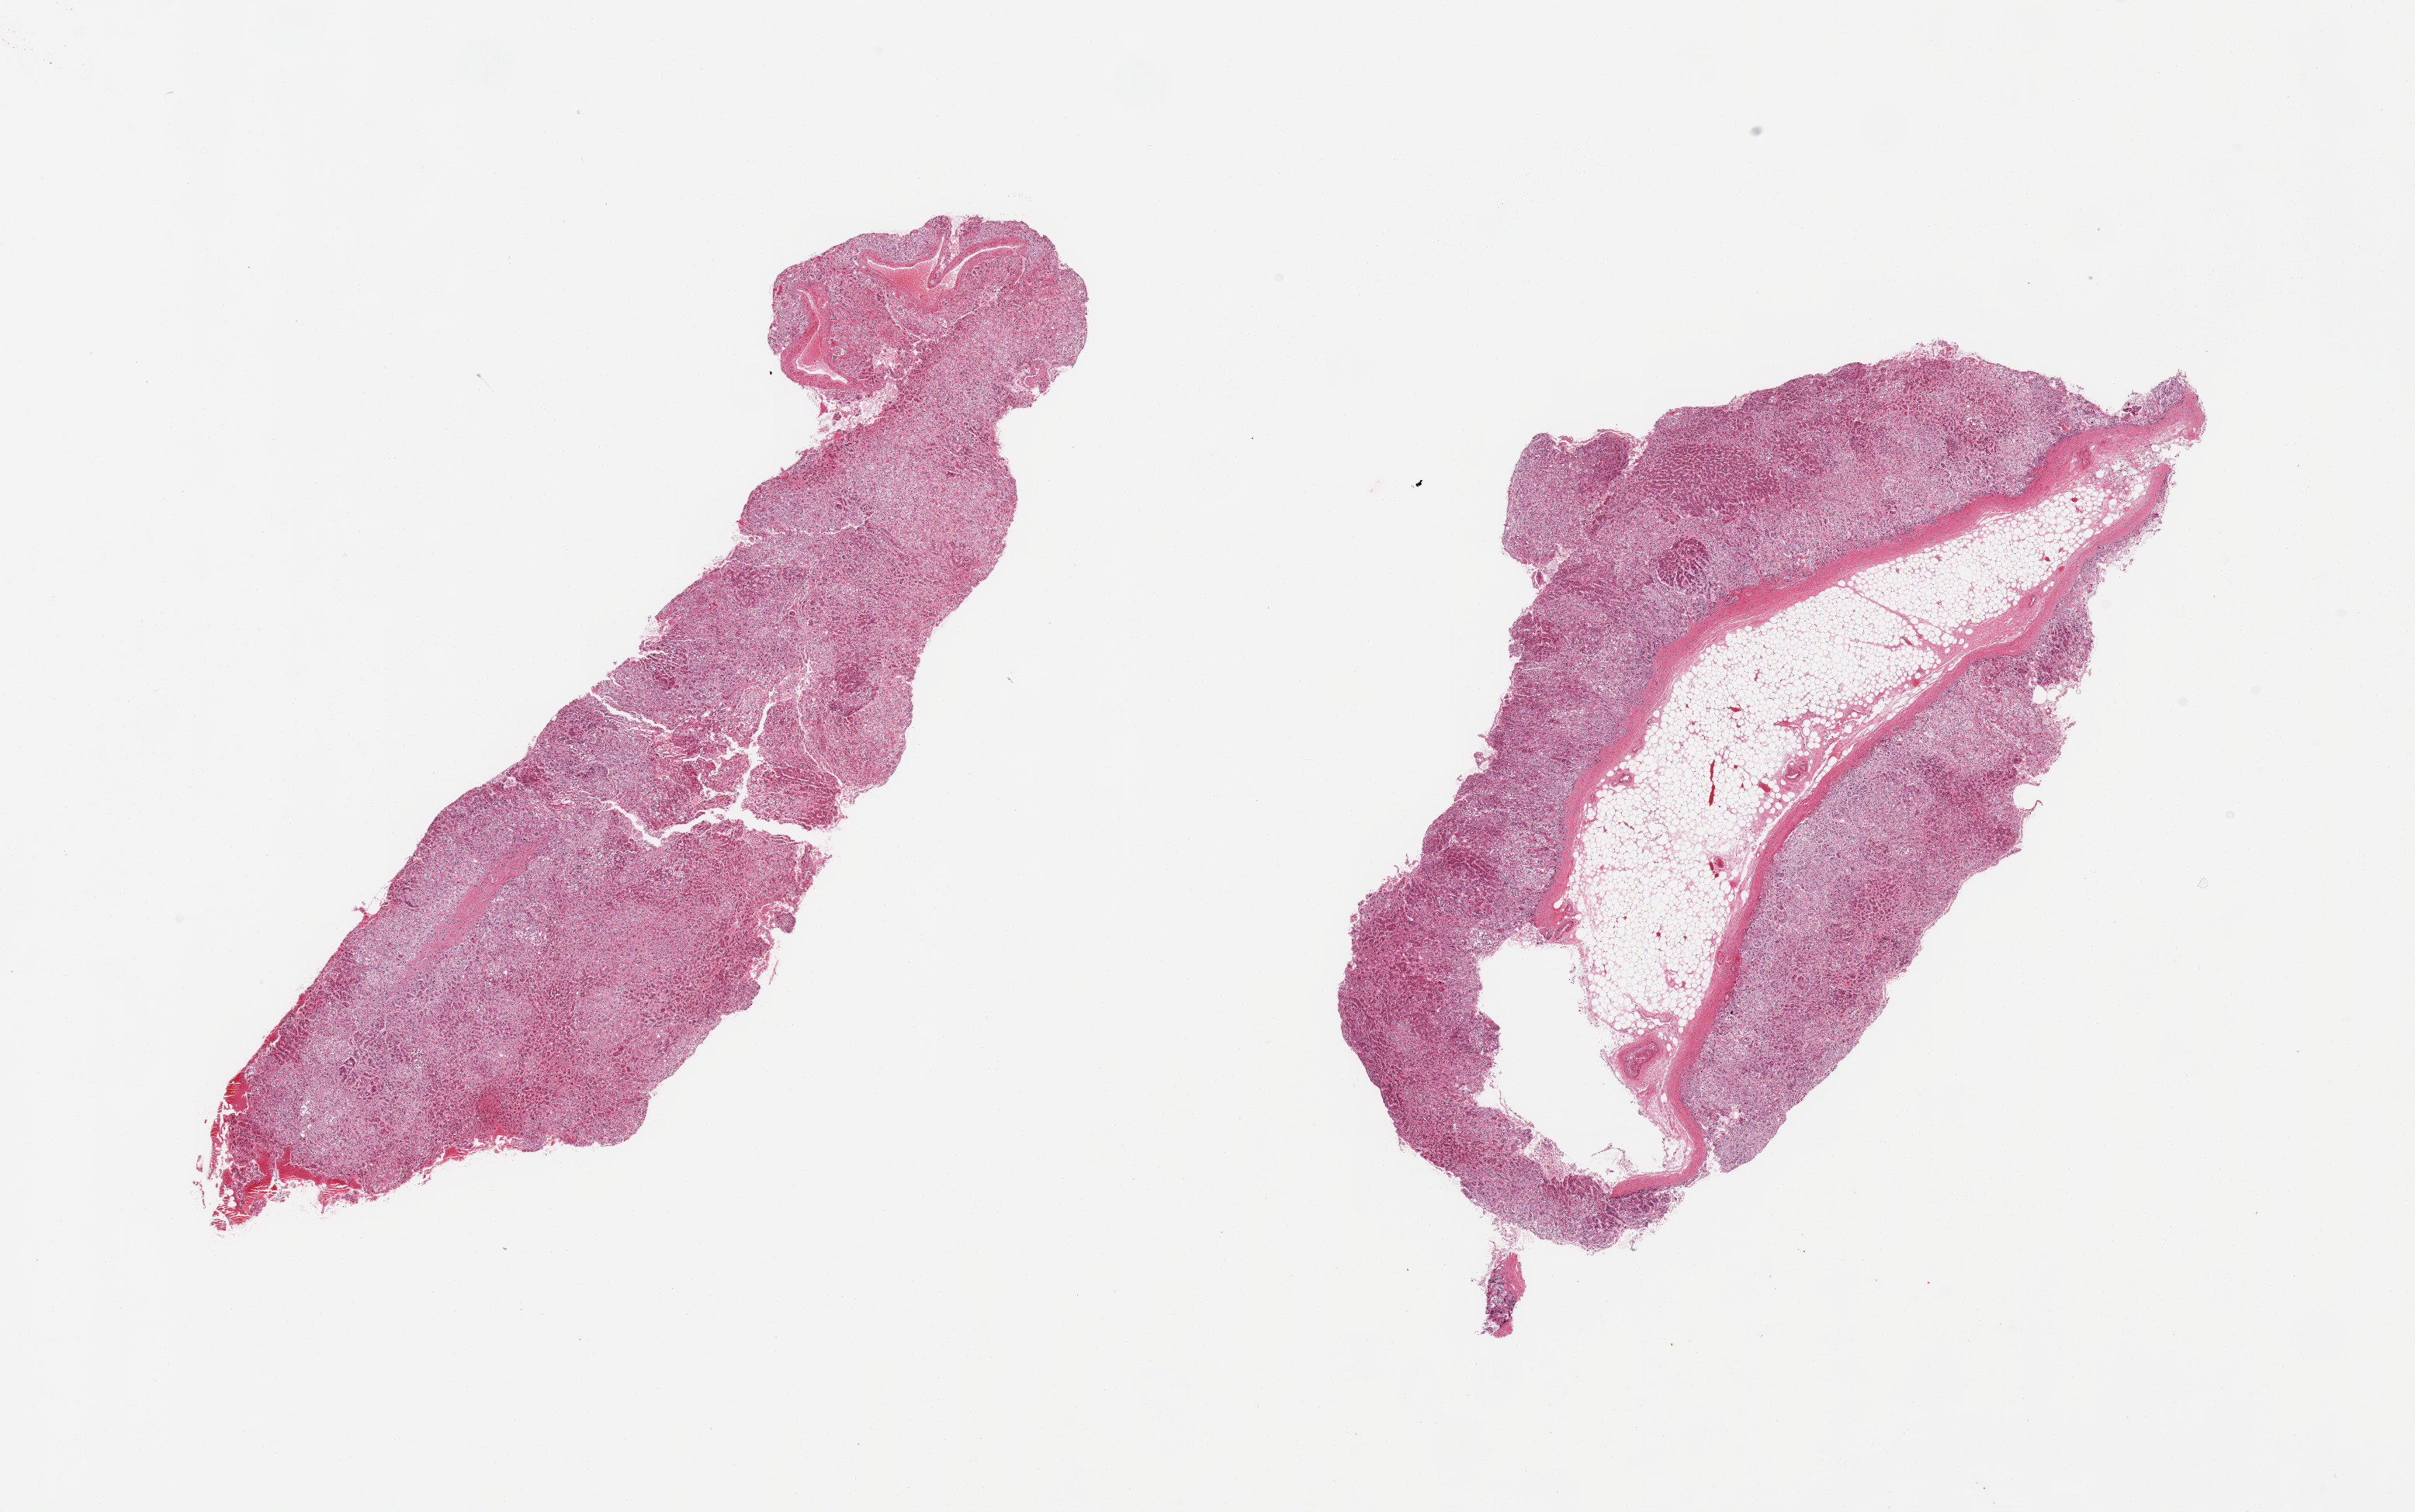
Digitized haematoxylin and eosin-stained section — whole scanned area (about 24.6 x 15.4 mm, slide scanned at 20x) shown as a low-resolution overview, PAXgene-fixed, paraffin-embedded tissue, section of adrenal gland (target tissue), donor tissue sample. Donor sex: male.
- reviewer comment on this tissue sample: 2 pieces, cortex, ~30% fat